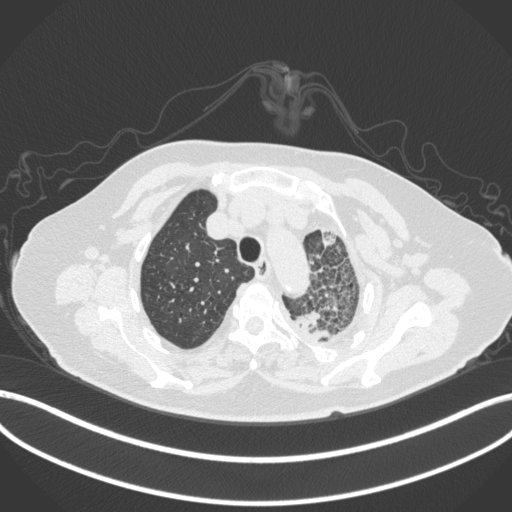
Chest CT, one axial slice; slice 320 of 399 in the series (ordered by position); reconstruction kernel B31f; lung window (W 1500 / L -600 HU); 1 mm slice thickness; 512 × 512 image matrix, field of view 400 × 400 mm. Patient: female, 75 years. Case-level facts recorded for this patient, not image findings: clinical TNM (as recorded): T3 N3 M1.
Annotated regions visible in this slice (bounding box drawn by a radiologist):
- lung tumour (recorded histology: adenocarcinoma): box from (x=287, y=306) to (x=329, y=346) px